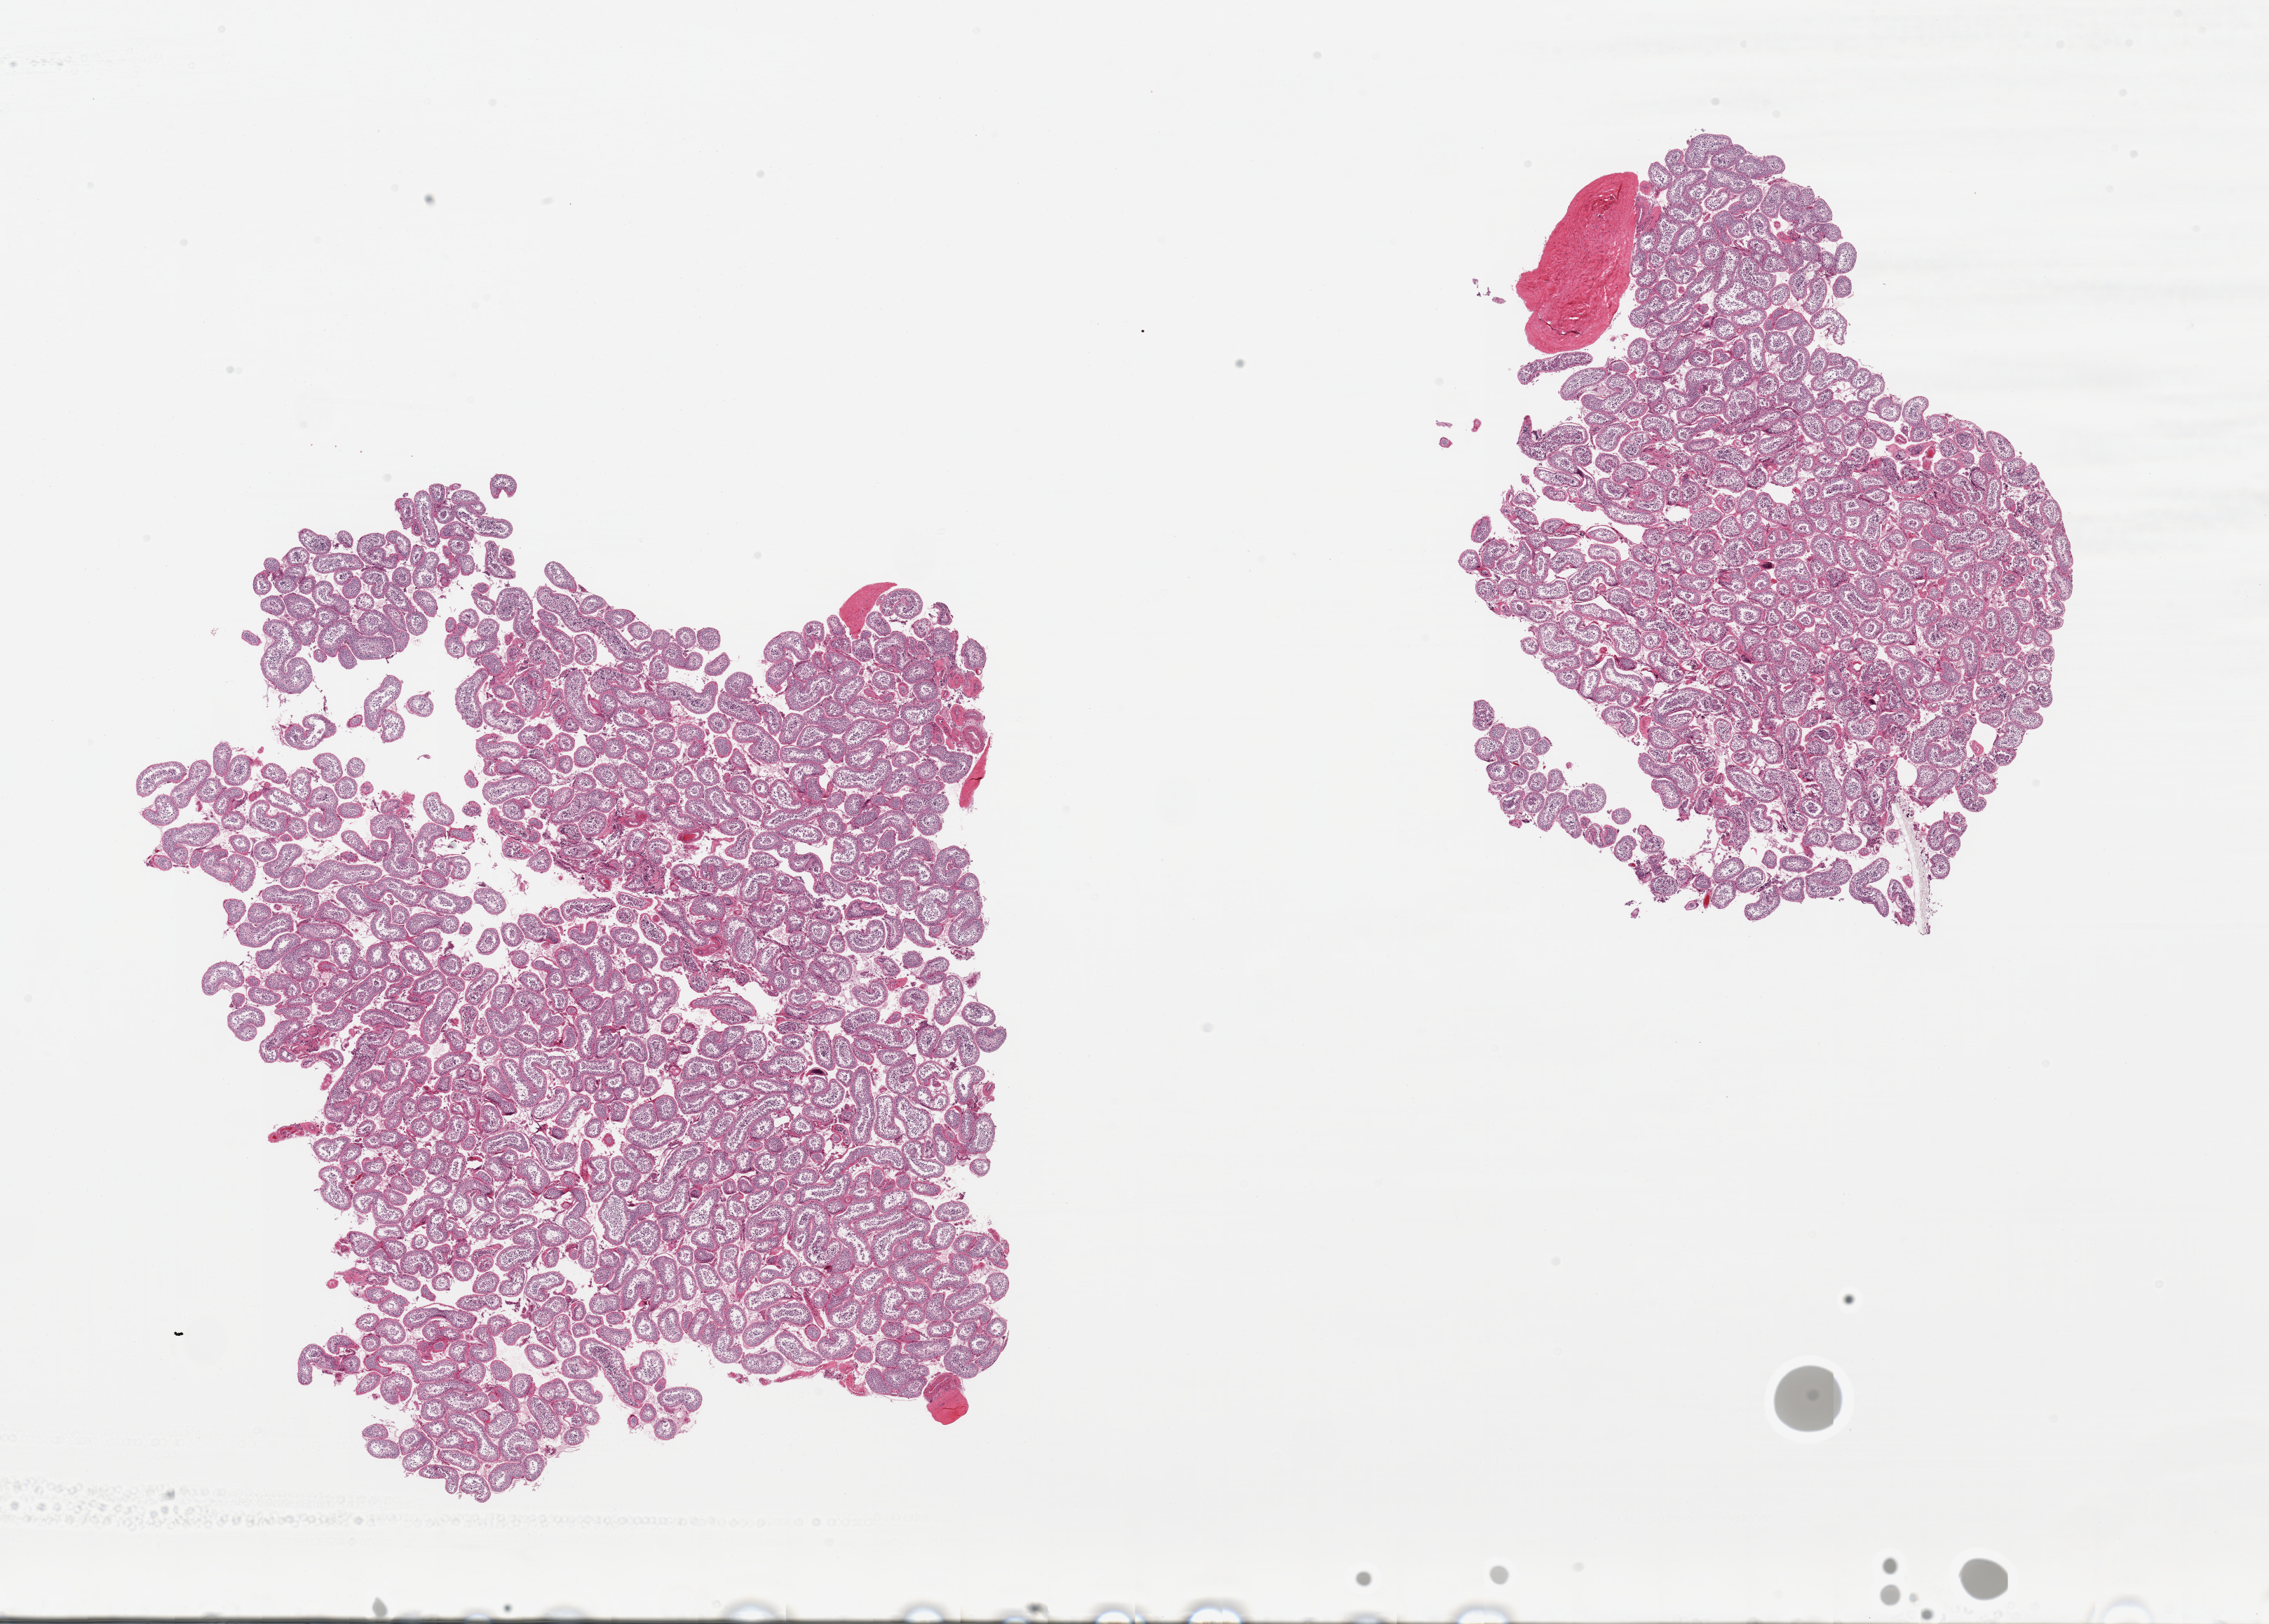
Digitized haematoxylin and eosin-stained section — low-resolution overview of the scanned area, about 25.6 x 18.3 mm (from a 20x scan). PAXgene-fixed paraffin-embedded (PFPE) section. Sampled site (target tissue): testis. Tissue donor sample. Donor sex: male.
* review note (as recorded): 2 pieces; spermatogenesis is present, portion of tunica albuginea present